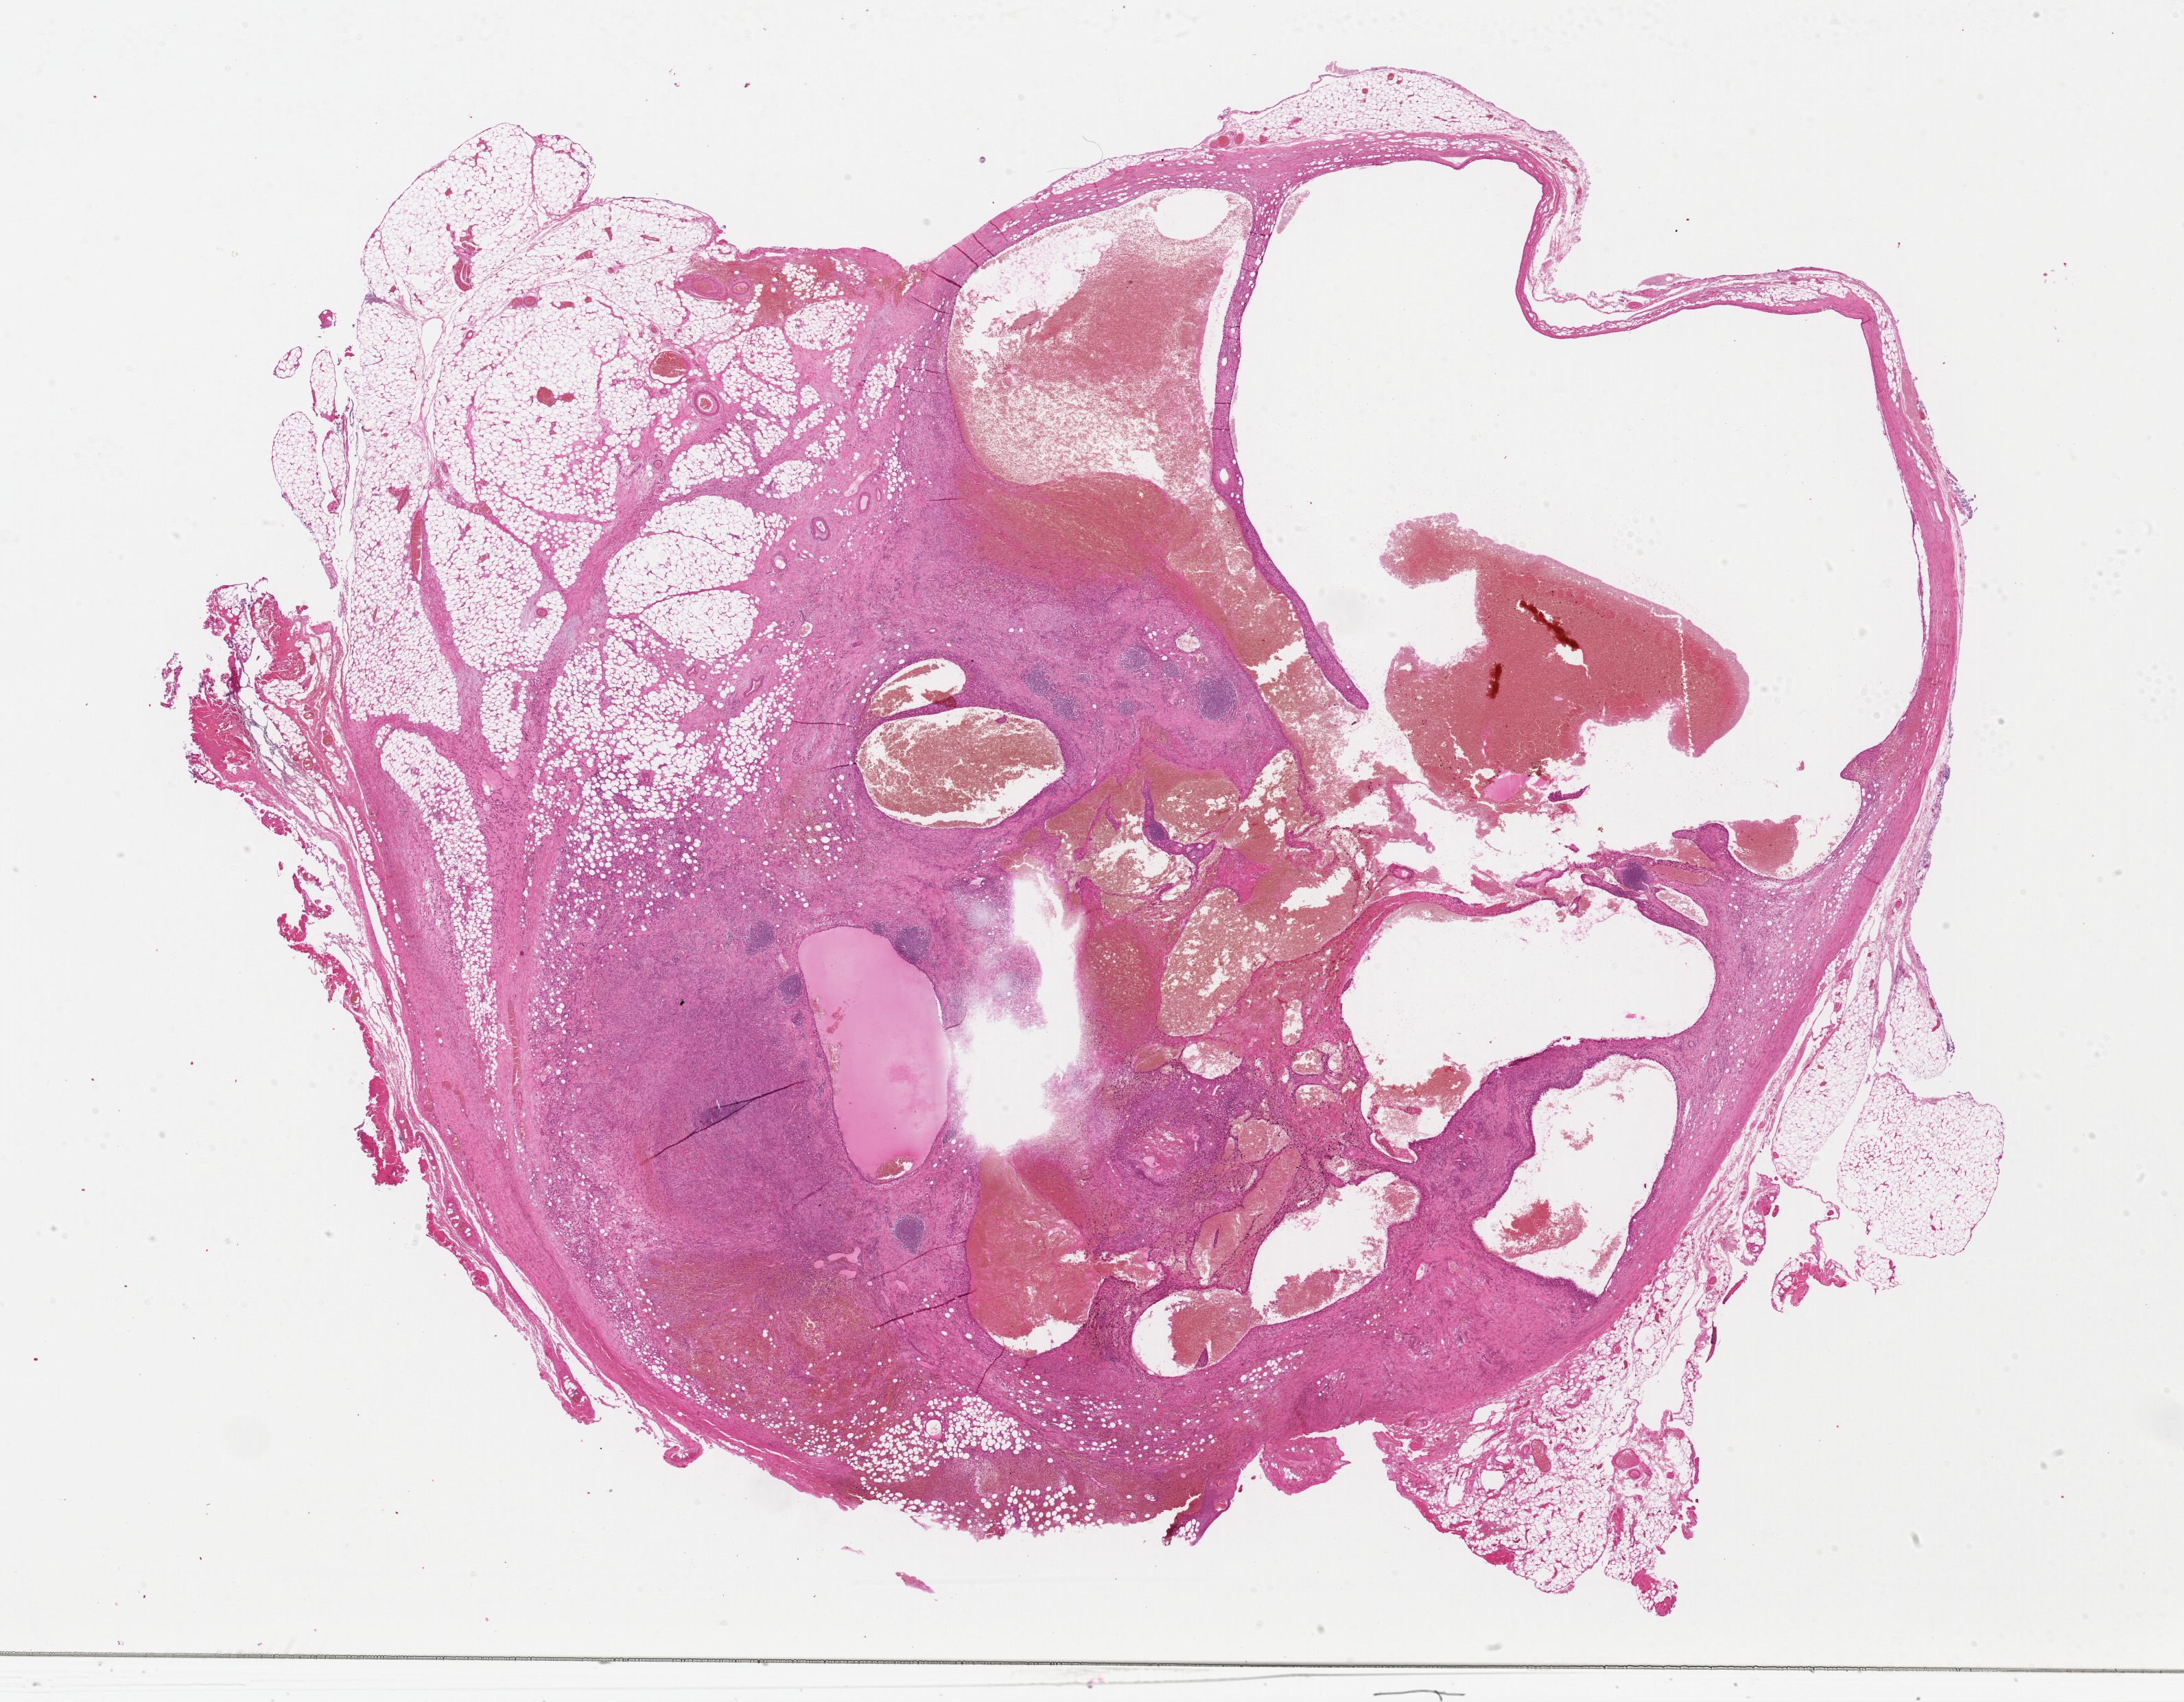
Hematoxylin and eosin (H&E) stained whole-slide image — whole scanned area (about 25.0 x 19.5 mm, from a 40x scan) shown as a low-resolution overview. Formalin-fixed paraffin-embedded (FFPE) diagnostic section. Primary tumour sample from the skin. Patient: male, age at initial diagnosis 66 years.
Histologic diagnosis: Malignant melanoma, NOS.